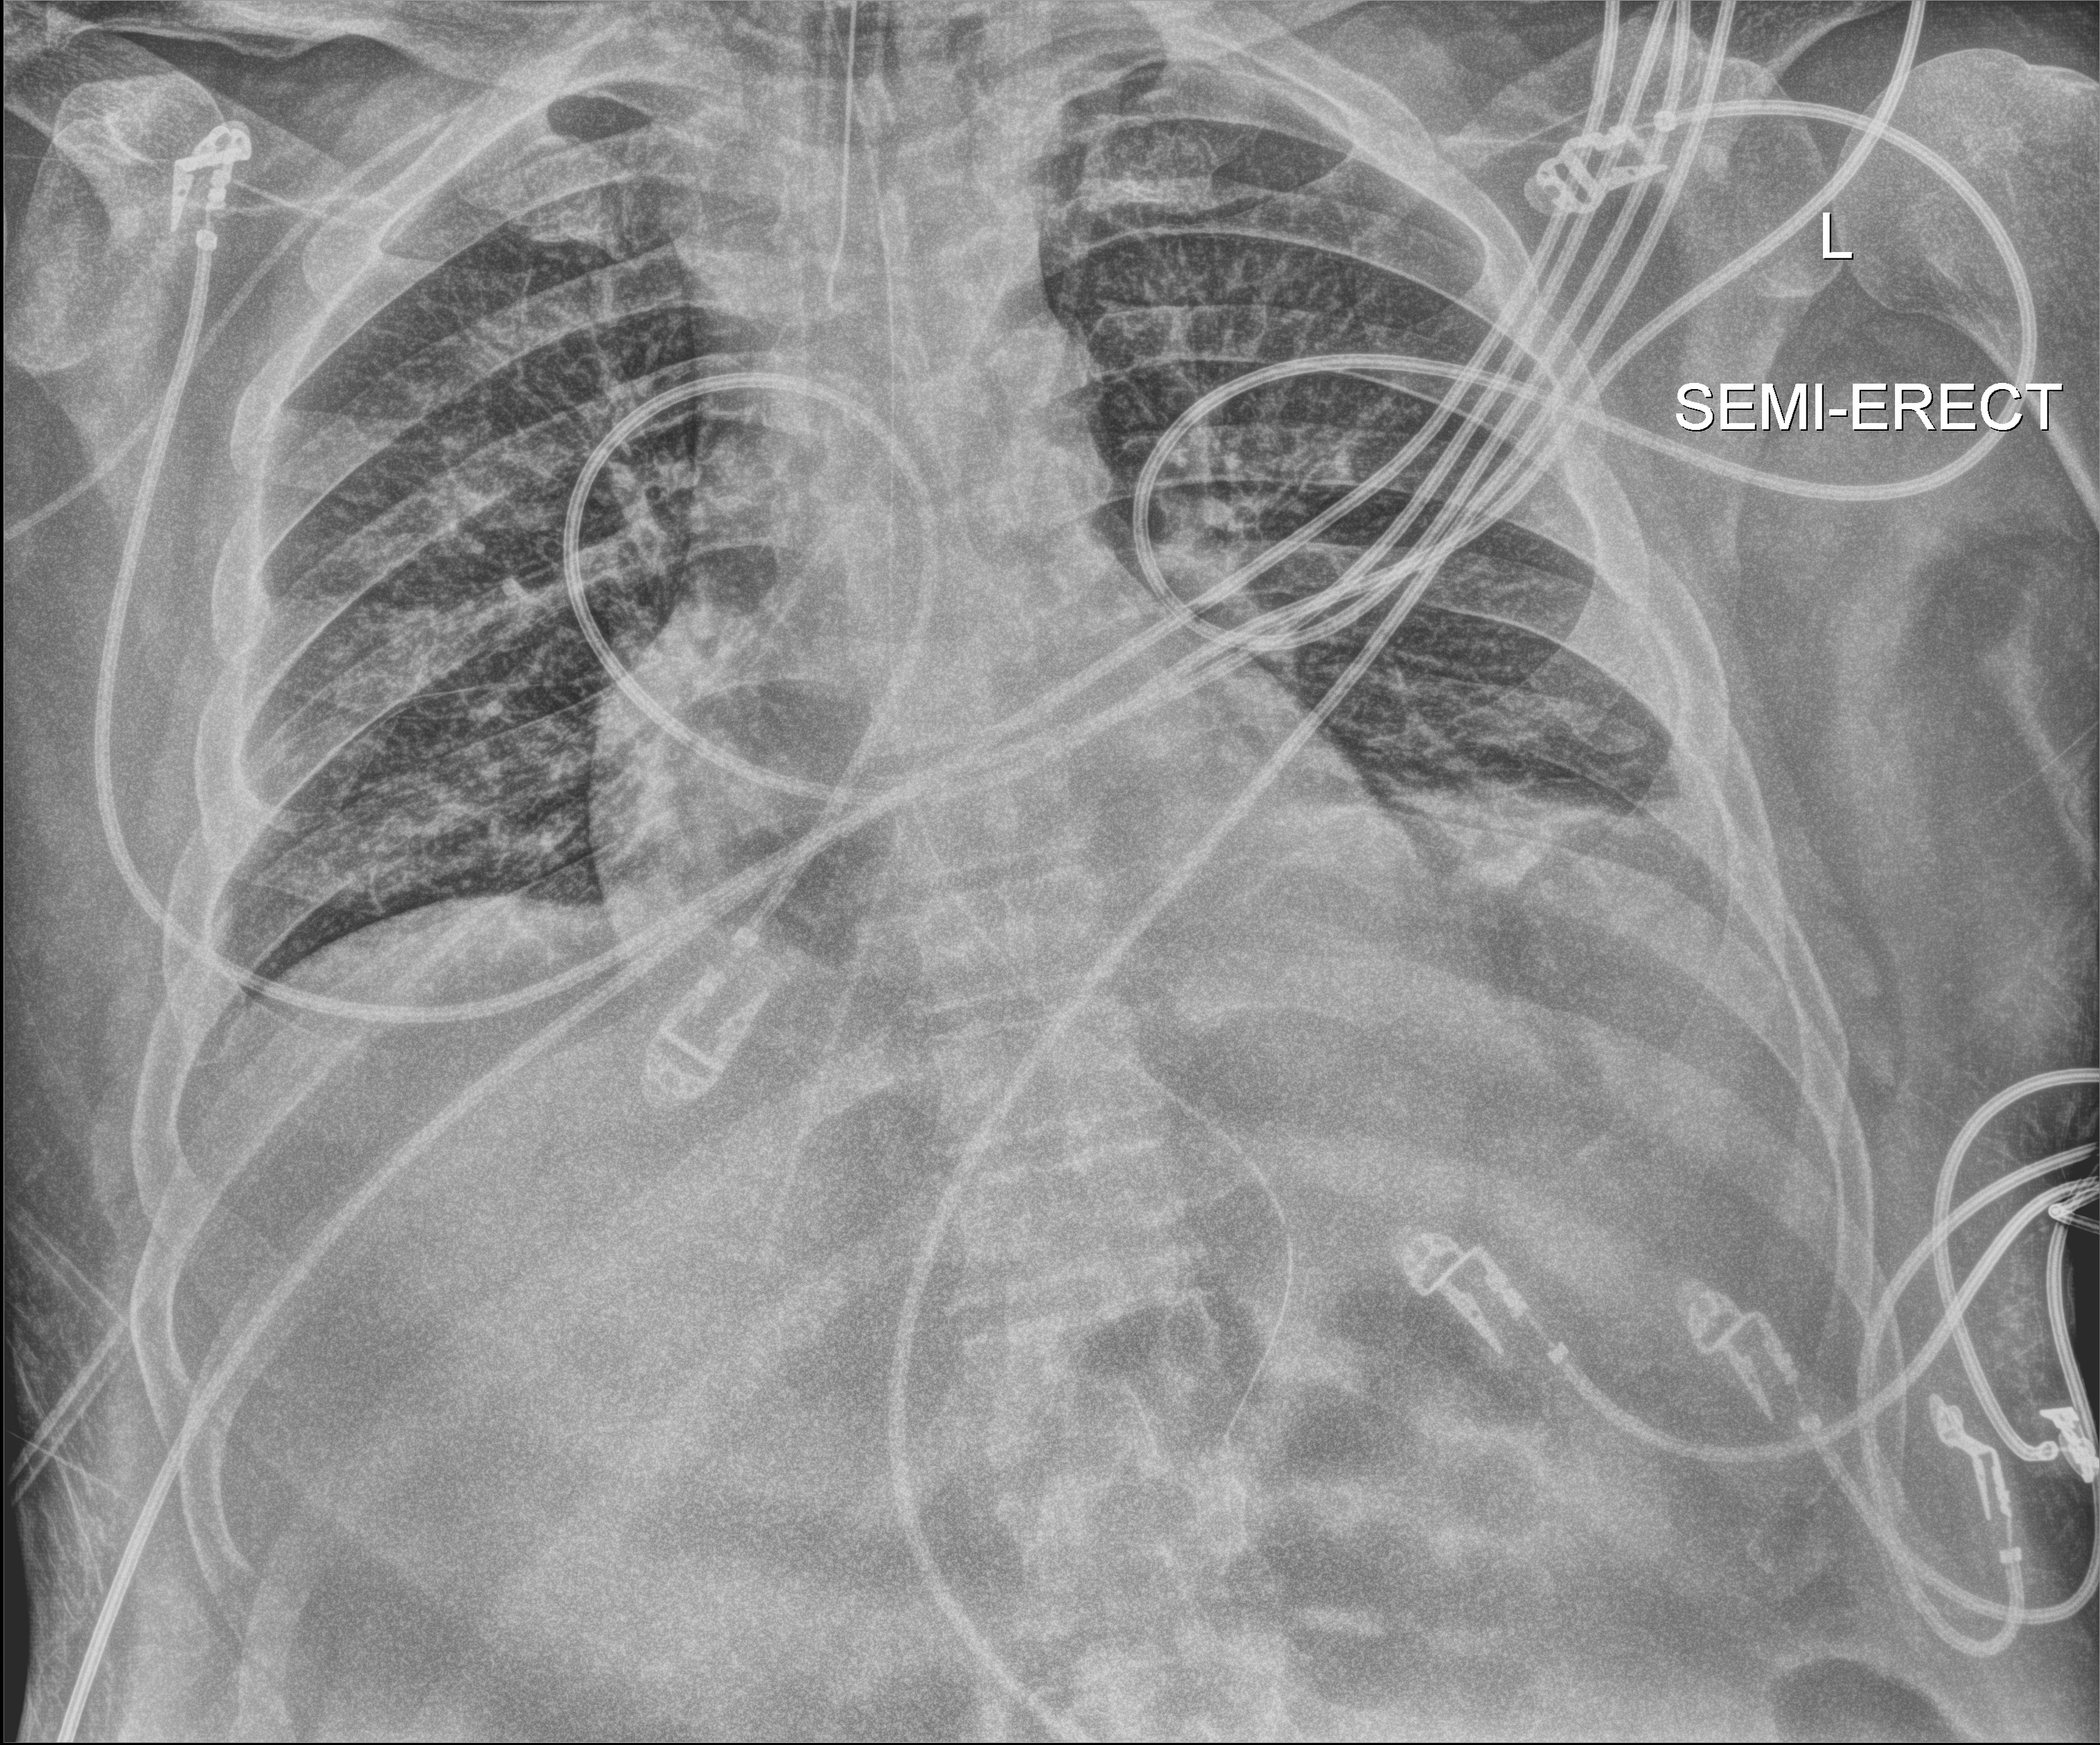
Portable chest radiograph; anteroposterior (AP) projection. Patient hospitalised with COVID-19; male, aged 18–59 years.
Admission-level facts for this patient (not findings on this image; timing relative to this image not recorded): admitted to intensive care during this hospital stay: yes; length of hospital stay: 65 days; mechanically ventilated during this hospital stay: yes.